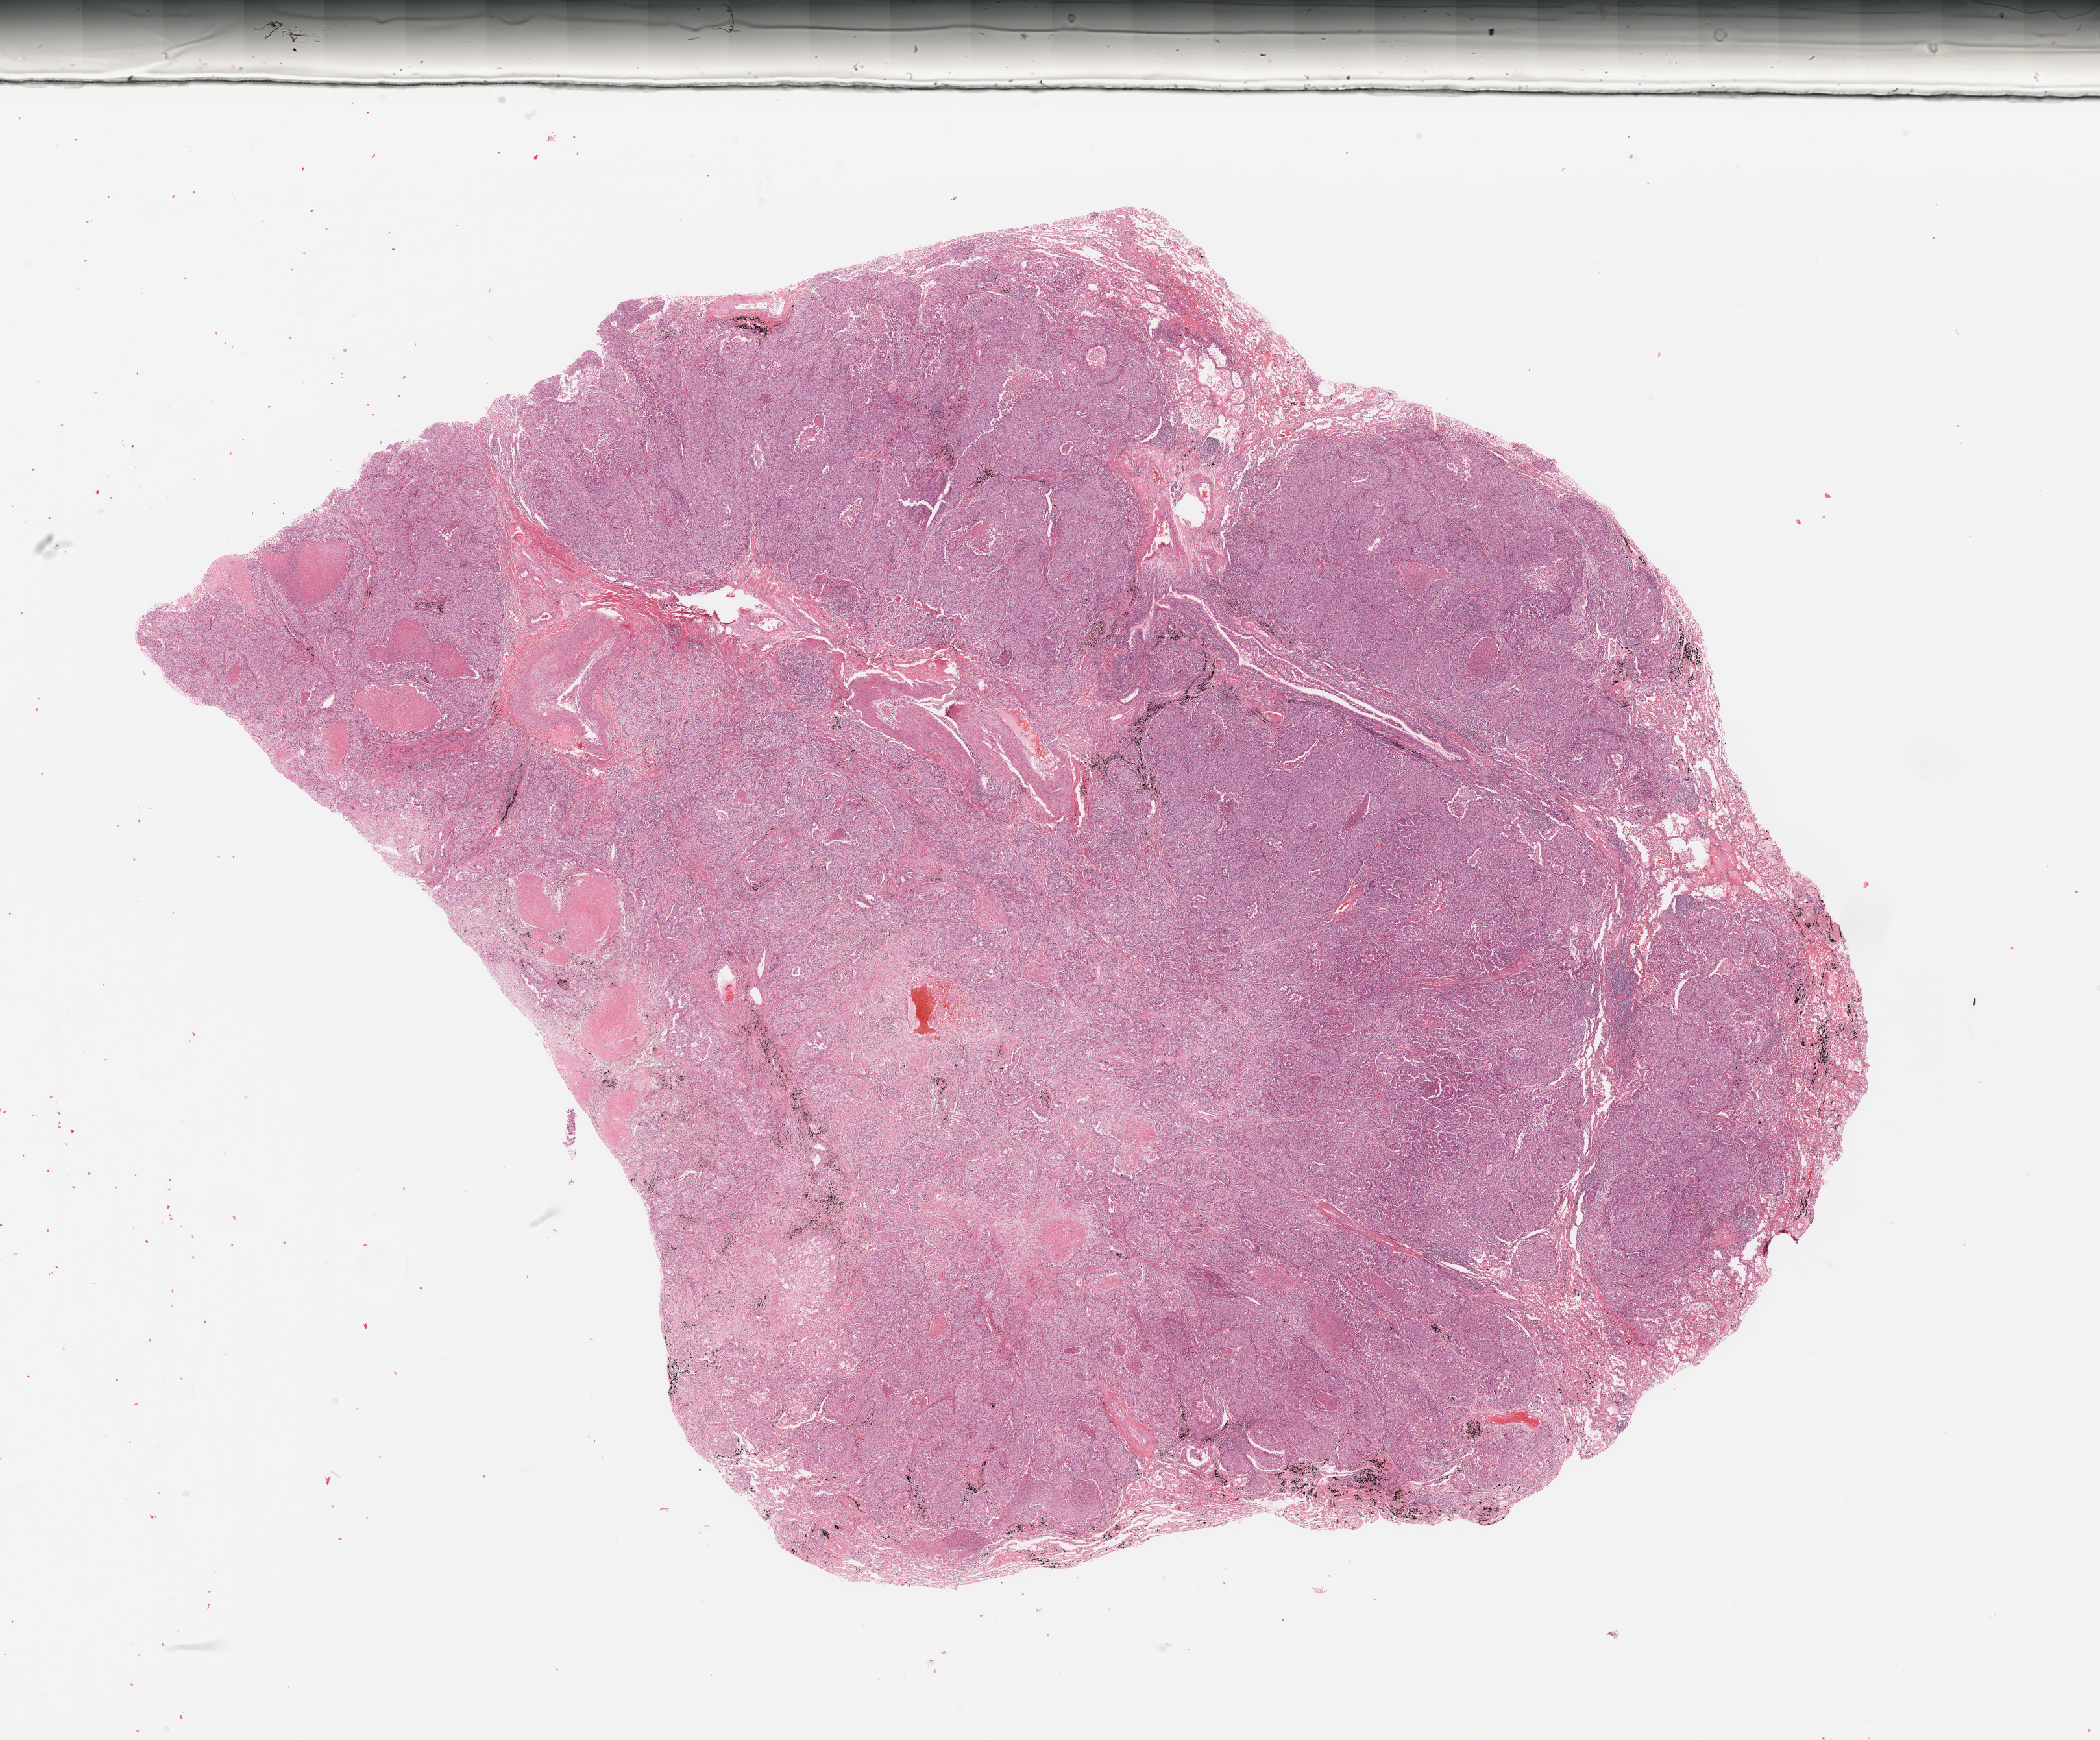
Digitized Hematoxylin and eosin (H&E) stained tissue section (whole slide), low-resolution overview of the scanned area, about 25.6 x 21.2 mm (from a 20x scan), tumour tissue sample, sampled site: lung. 55-year-old male patient. Histologic grade: G3 (poorly differentiated). Slide review estimates, as recorded: tumour nuclei 80%, necrosis 15%.
- histologic diagnosis: Adenocarcinoma, NOS
- AJCC pathologic stage: IIIA